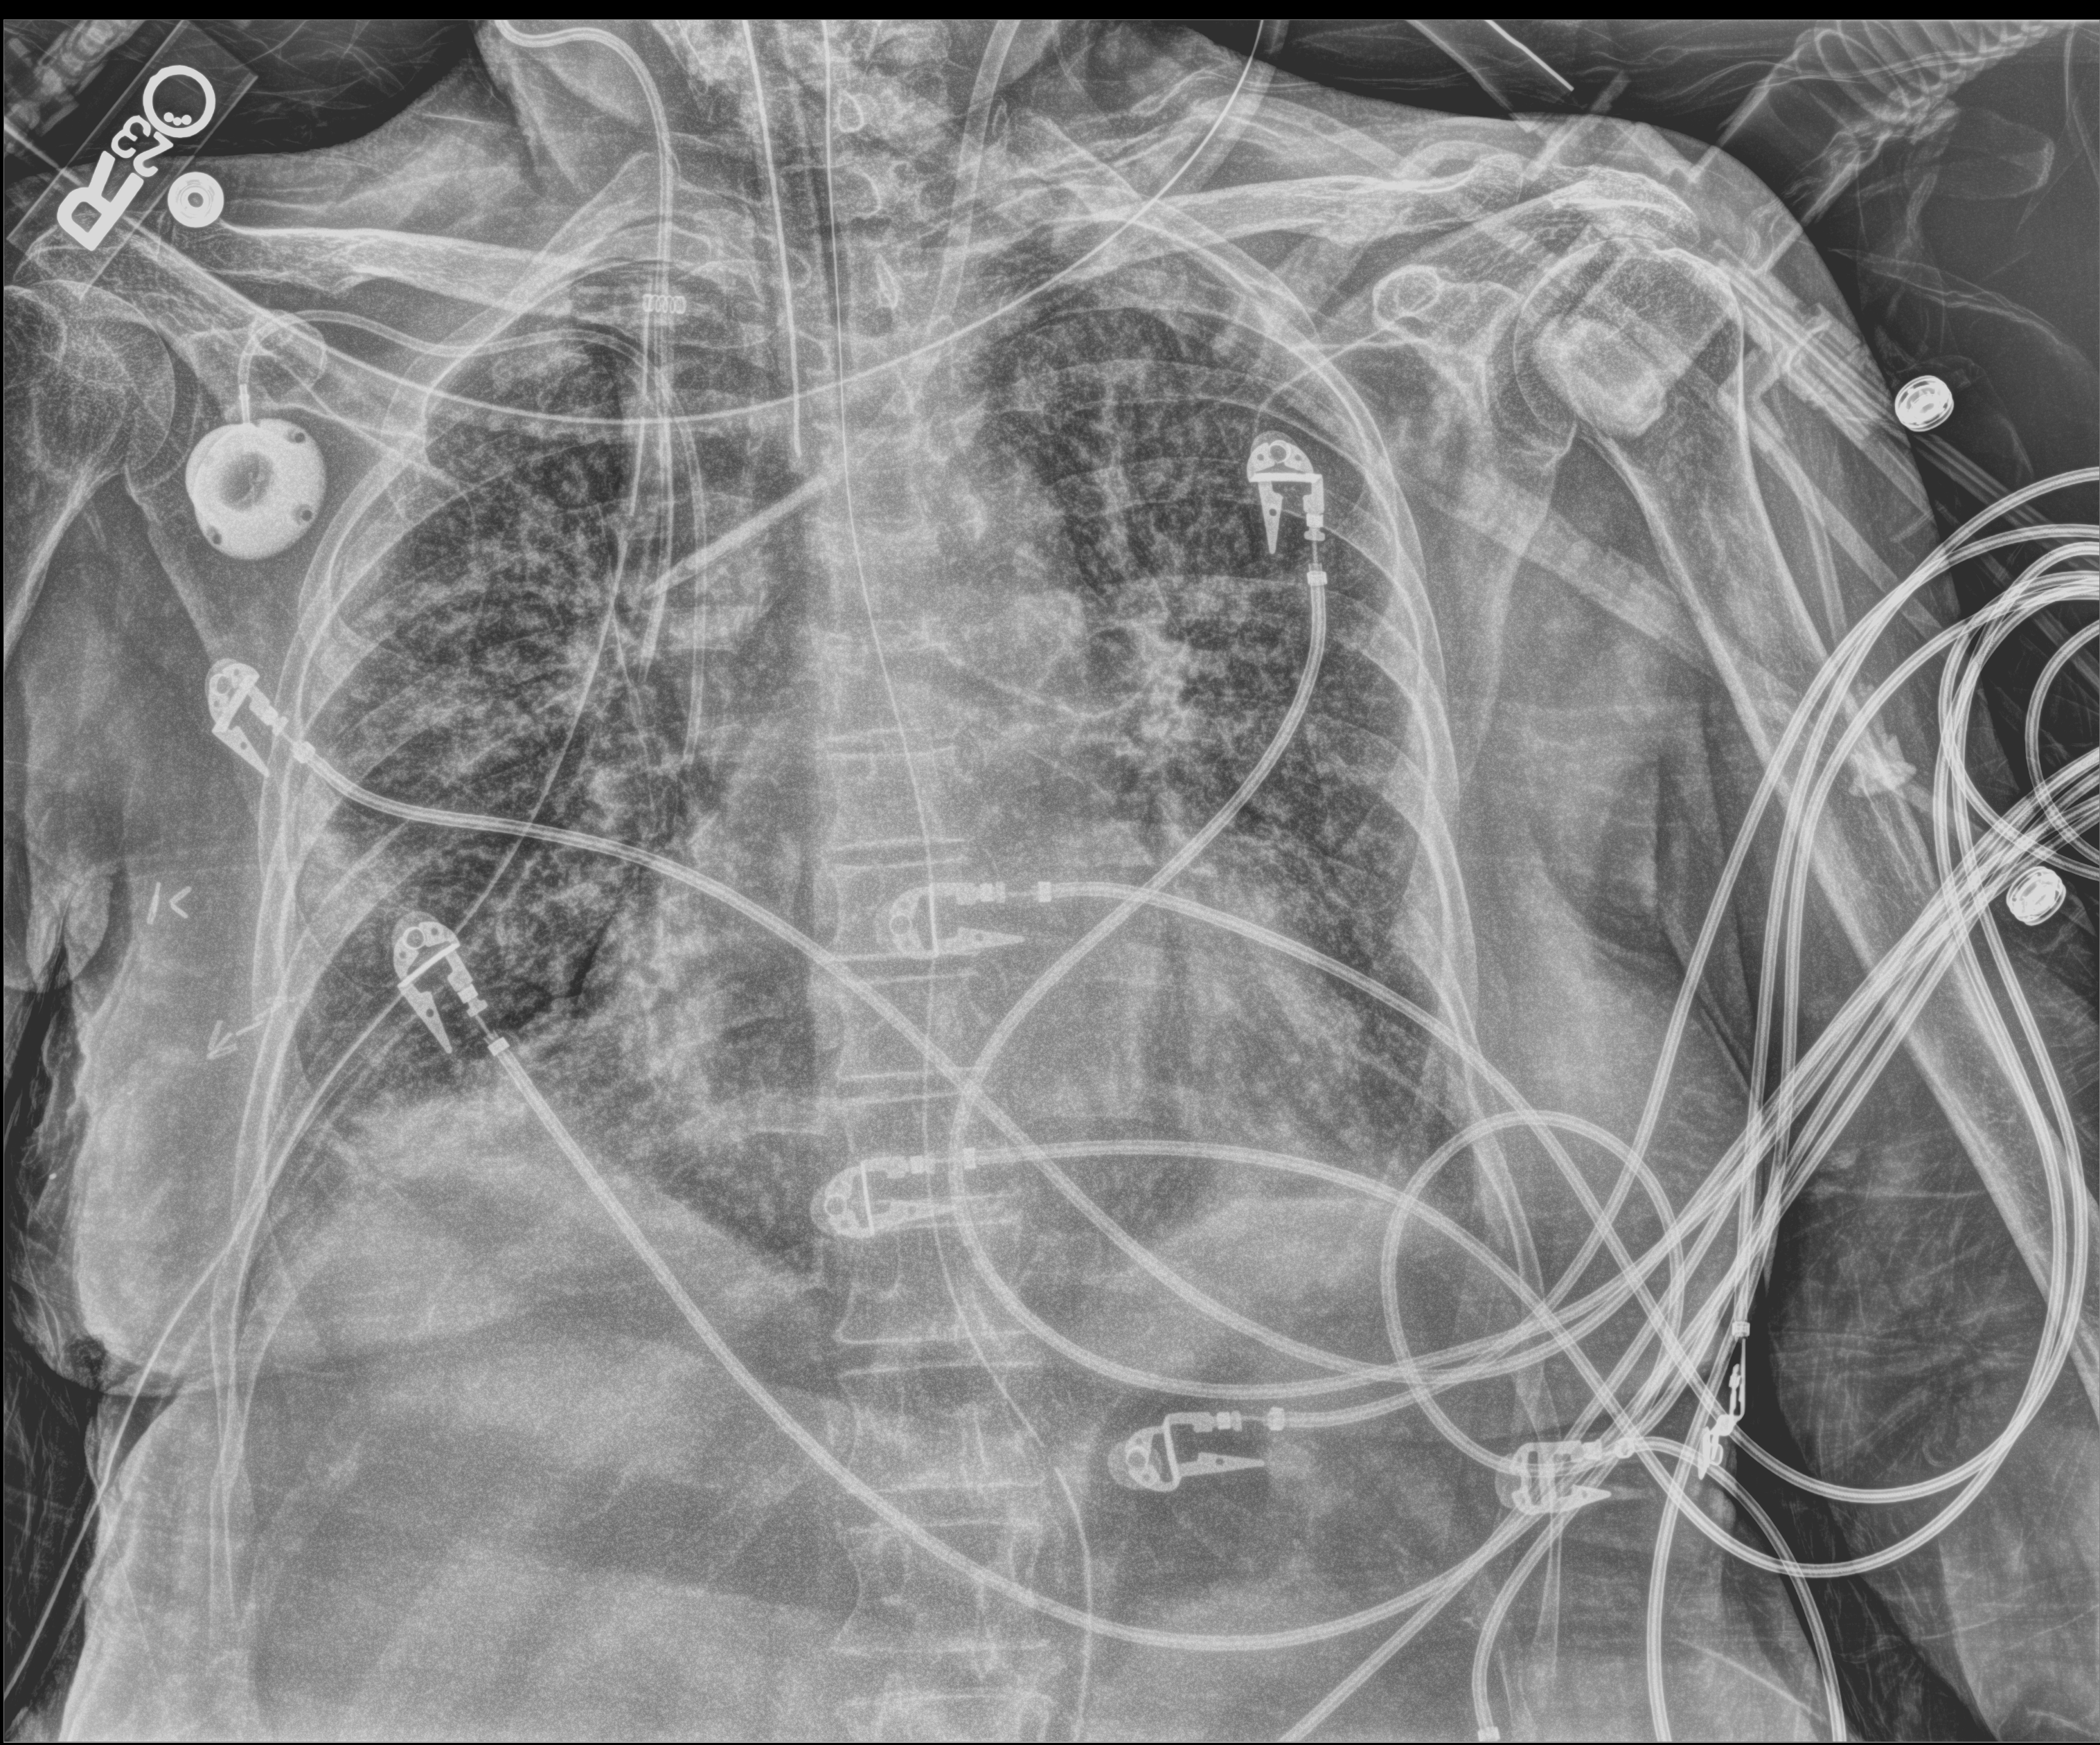
Bedside chest radiograph (digital radiography), anteroposterior (AP) projection. Patient hospitalised with COVID-19; female, aged 60–74 years.
Hospital-stay facts (about this admission, not read from this image; timing relative to this image not recorded): admitted to intensive care during this hospital stay: yes; mechanically ventilated during this hospital stay: yes; other chronic lung disease (admission record): no.